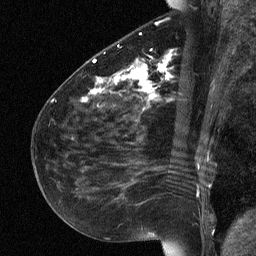
Breast MRI (dynamic contrast-enhanced), one sagittal slice. Slice 30 of 64 in the series (ordered by position). Dynamic contrast-enhanced study with each time point stored as its own series, time point 2 of 3 at this slice position (early post-contrast, ordered by acquisition time). 1.5 T. TE 4.8 ms, TR 27 ms. 2 mm slice thickness. 256 × 256 image matrix, field of view 180 × 180 mm. Patient: female, 51 years. Case-level facts recorded for this patient, not image findings: setting: breast cancer imaged before/during neoadjuvant chemotherapy; receptor status: HR-positive, HER2-negative.
Annotated regions visible in this slice (semi-automatic segmentation, software-assisted and operator-edited):
- analysis volume of interest (the breast-tissue region the enhancement analysis was run in; not a lesion): box from (x=72, y=34) to (x=182, y=118) px
- tumour enhancement mask (voxels above the 90 % enhancement threshold inside the analysis volume of interest): (x=81, y=60)–(x=167, y=102)